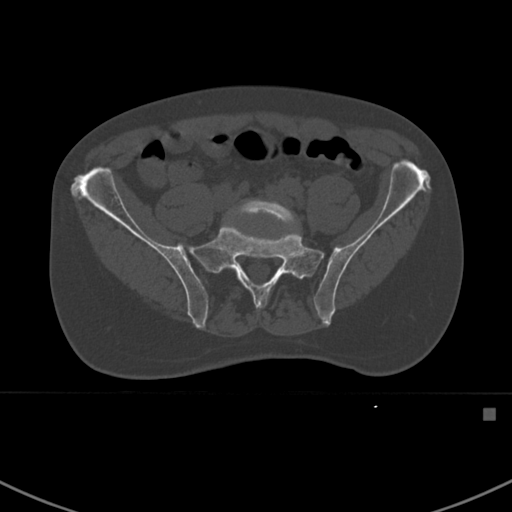
CT including the spine, one axial slice. Slice 205 of 412 in the series (ordered by position). 120 kVp. Bone window (W 1800 / L 400 HU). 1.5 mm slice thickness. 512 × 512 image matrix, field of view 358 × 358 mm. Male patient, age 59 years. From the clinical record (not read from this slice): primary cancer: prostate.
Outlined on this slice (semi-automatic segmentation, software-assisted and operator-edited):
- L5 vertebra: bounding box [x1, y1, x2, y2] px = [230, 199, 297, 229]